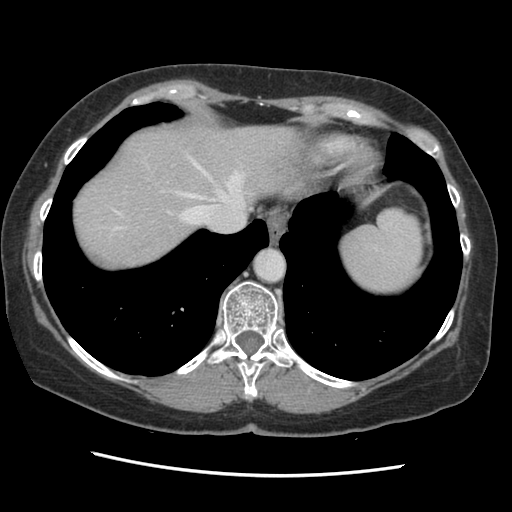
Contrast-enhanced abdominal CT, one axial slice. Slice 119 of 141 in the series (ordered by position). 120 kVp. Soft-tissue window (W 400 / L 40 HU). 512 × 512 image matrix. Female patient, age 61 years. From the clinical record (not read from this slice): diagnosis: colorectal cancer liver metastases, imaged before liver resection; multiple liver metastases: no; largest metastasis: 2.4 cm; disease in both lobes: no.
Outlined on this slice (manually delineated by an expert):
- hepatic veins: bounding box [x1, y1, x2, y2] px = [114, 156, 244, 224]
- liver: [71, 124, 301, 270]
- planned liver remnant (the part of the liver to remain after resection): [72, 124, 301, 270]